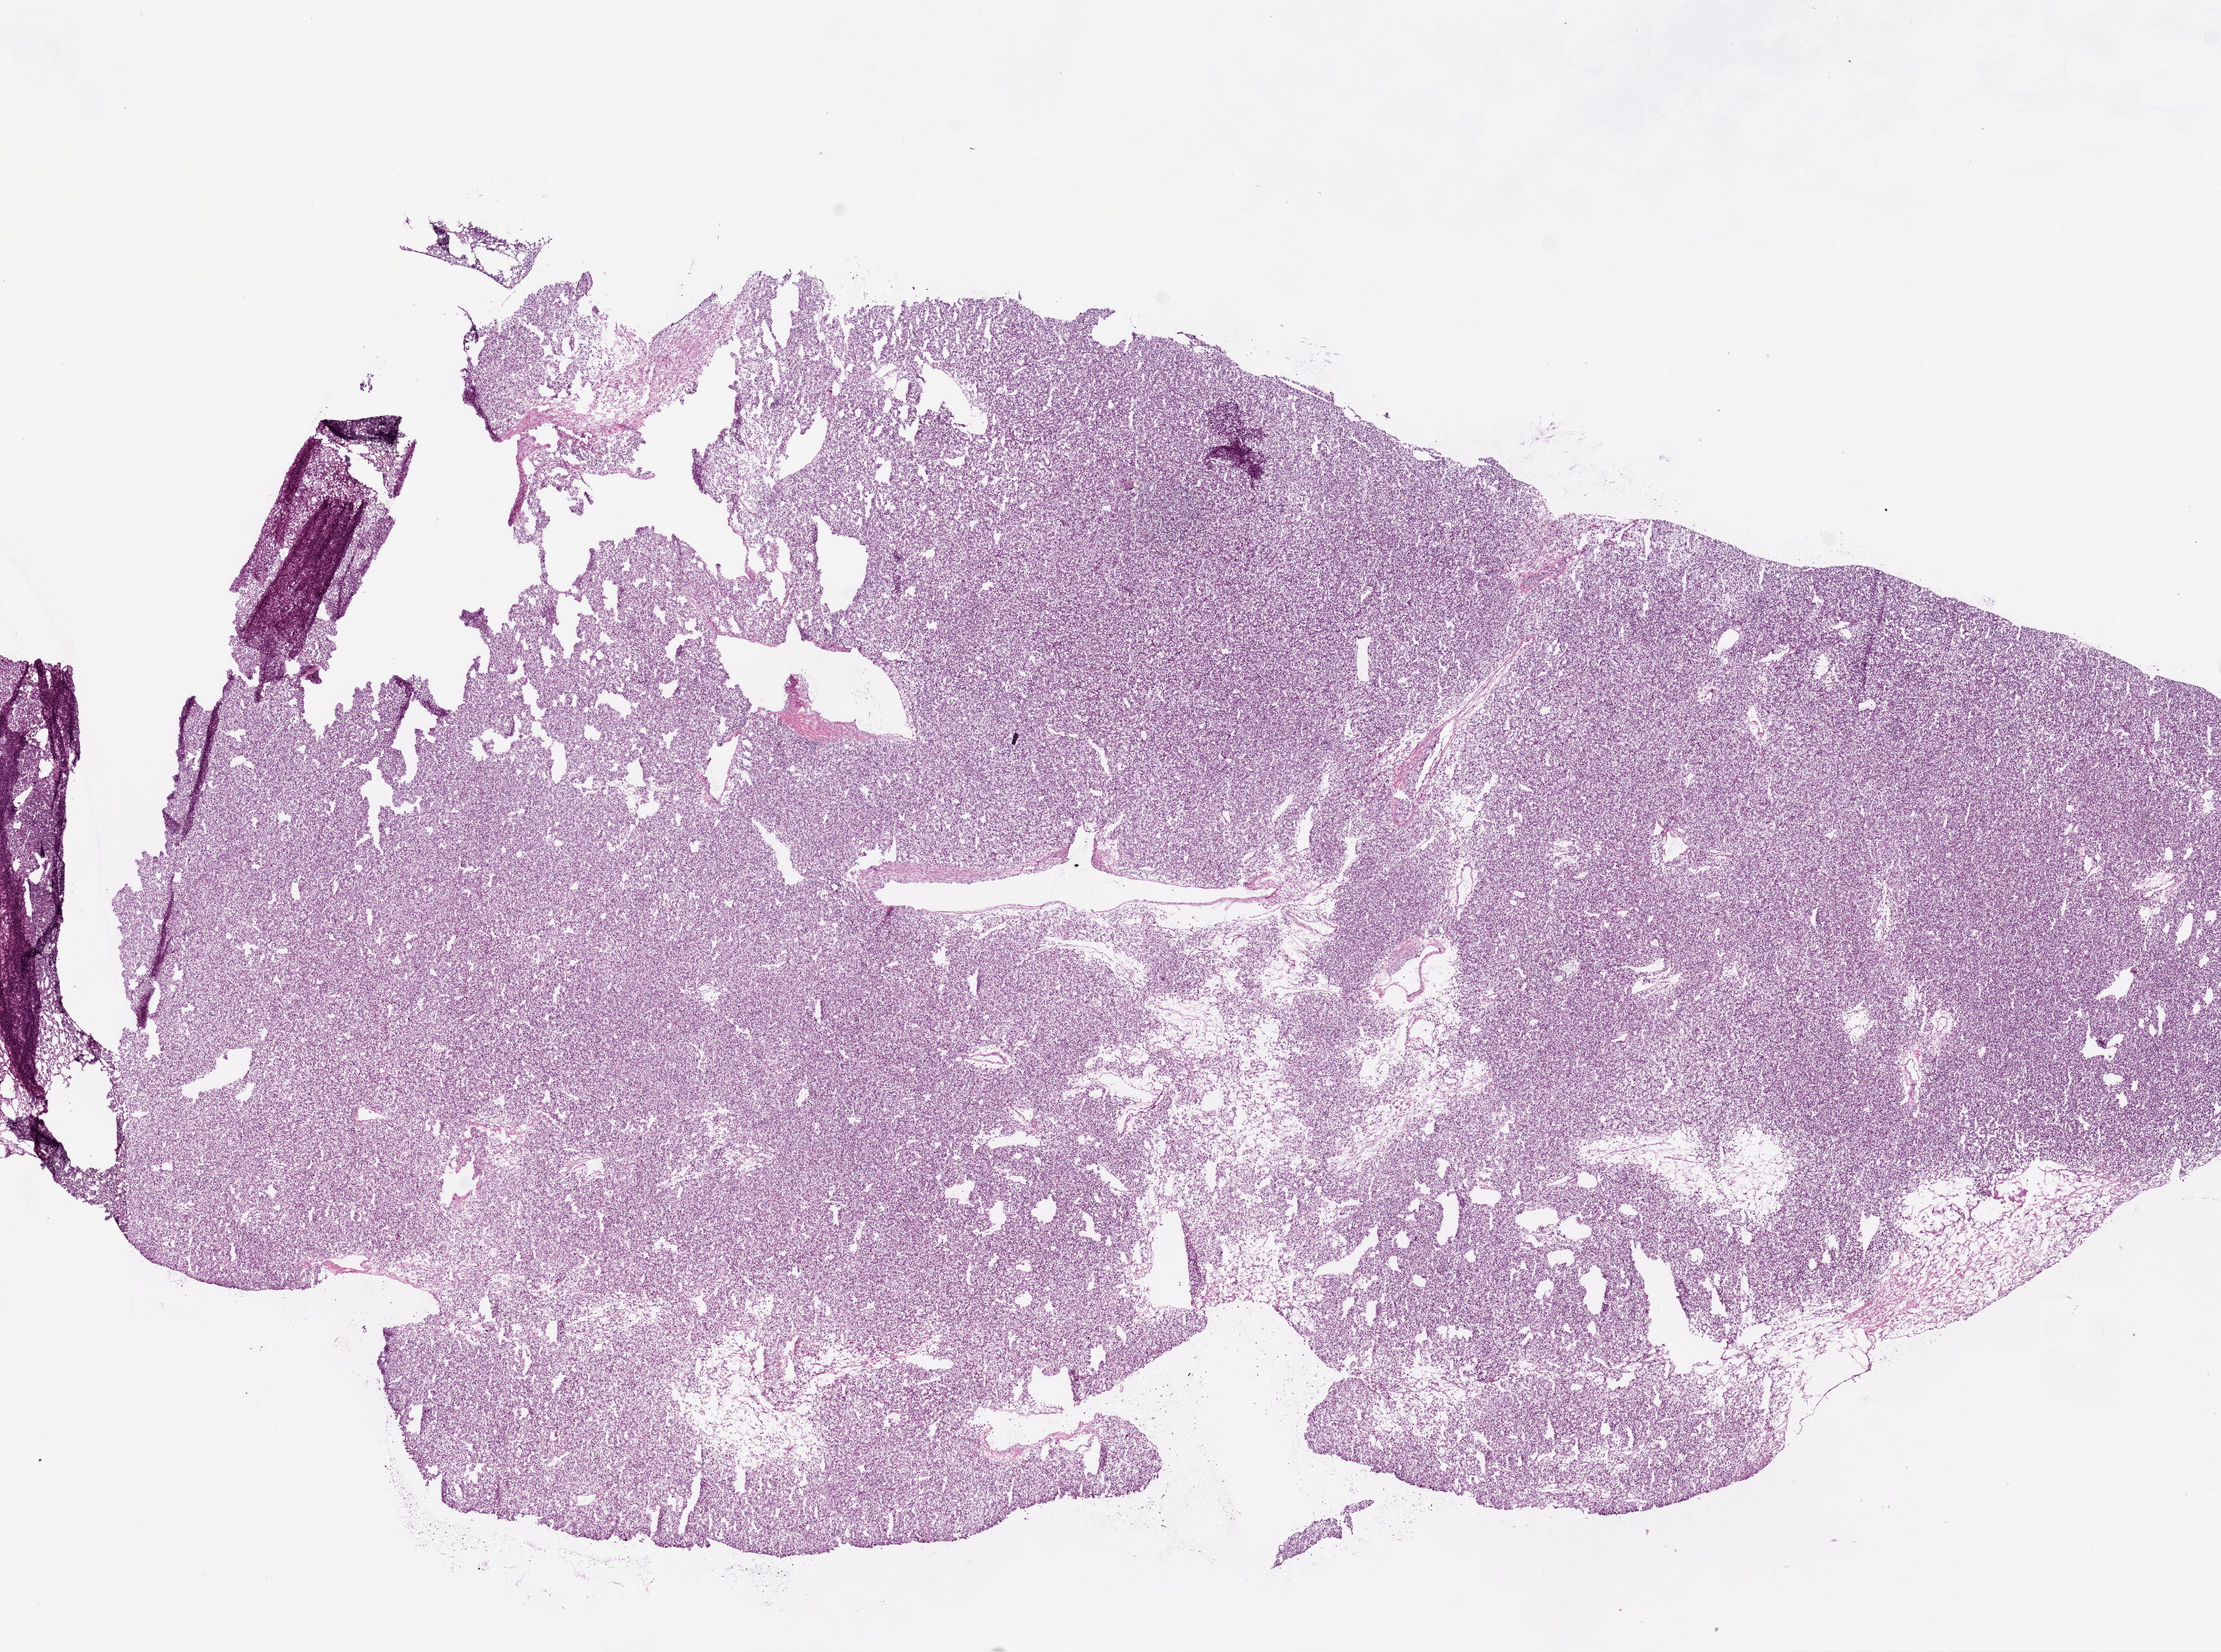
Digitized Hematoxylin and eosin (H&E) stained tissue section (whole slide) — whole scanned area (about 15.0 x 11.2 mm) shown as a low-resolution overview, frozen section, primary tumour sample from the kidney. Female, age 65 years at initial diagnosis. Histologic grade: G2 (moderately differentiated). Pathologist review of this section (percent, as recorded): tumour cells 90%, tumour nuclei 85%, normal cells 0%, stromal cells 10%, necrosis 0%.
AJCC pathologic stage: I. Diagnosis: Clear cell adenocarcinoma, NOS.